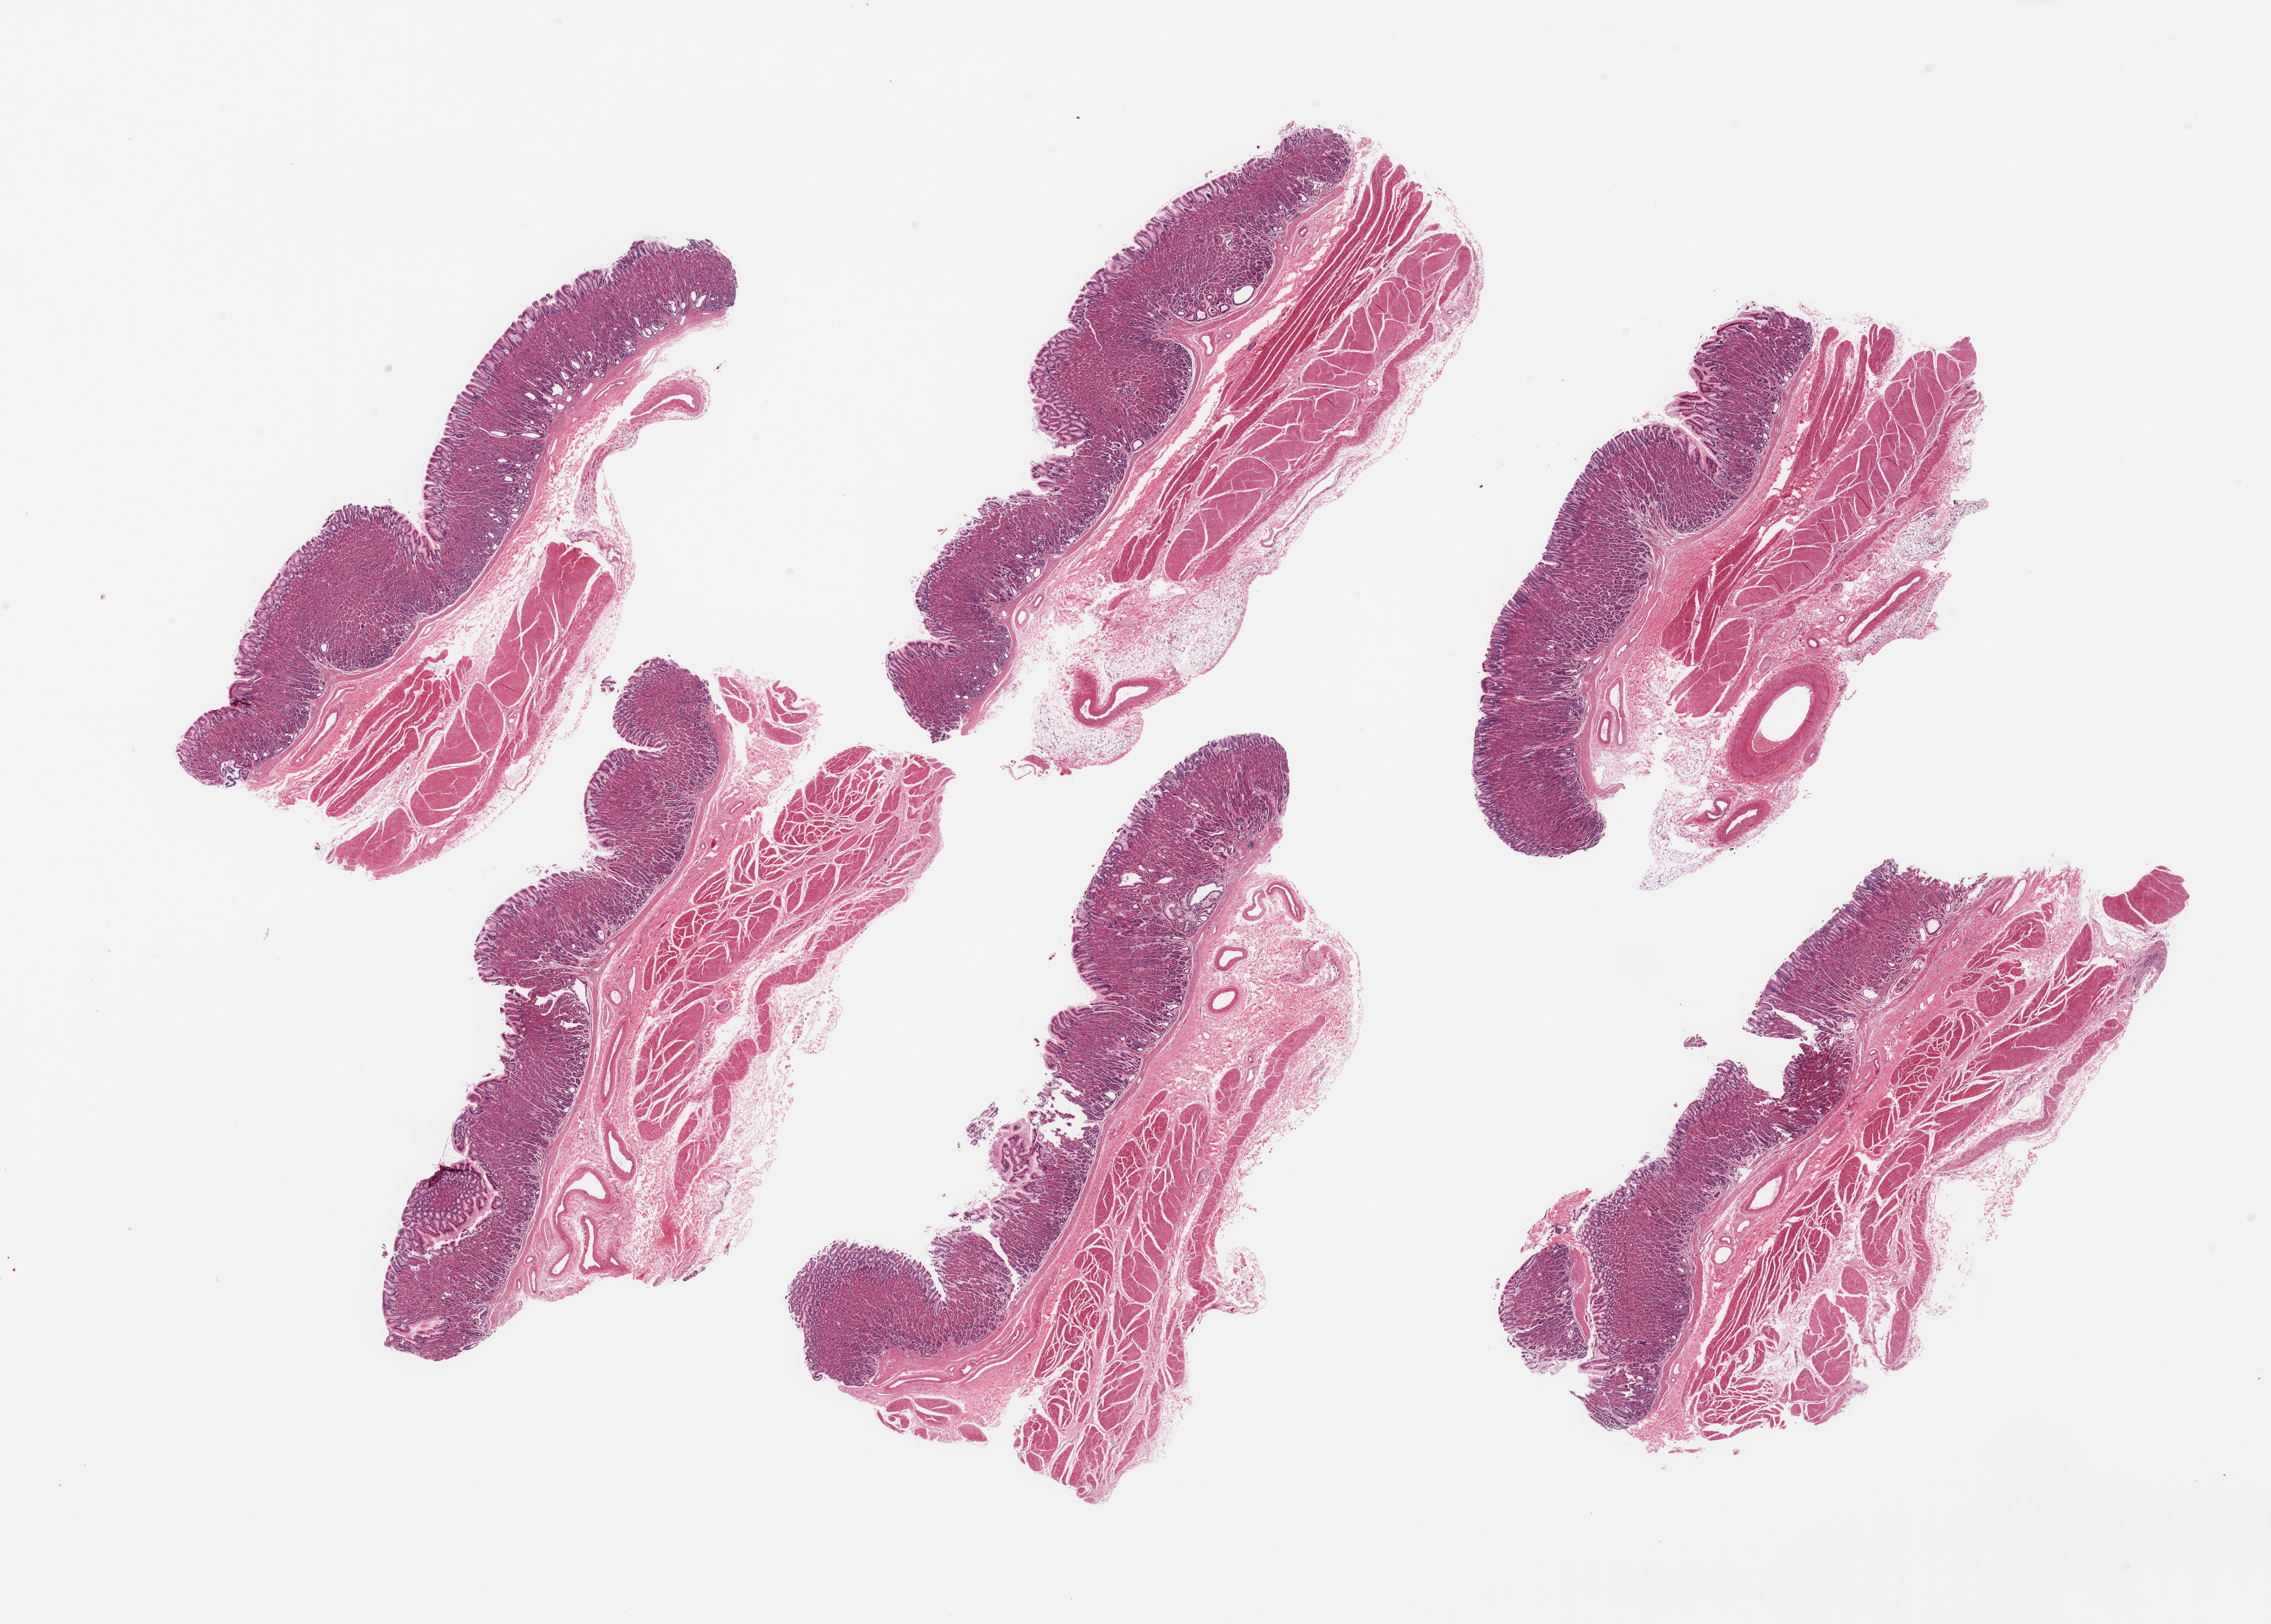
Whole-slide image, hematoxylin and eosin (H&E) stain — low-resolution overview of the scanned area, about 28.5 x 20.4 mm; PAXgene-fixed, paraffin-embedded tissue; sampled site (target tissue): stomach; donor tissue sample.
* review note (as recorded): 6 pieces; full thickness specimens; microcystic glandular change